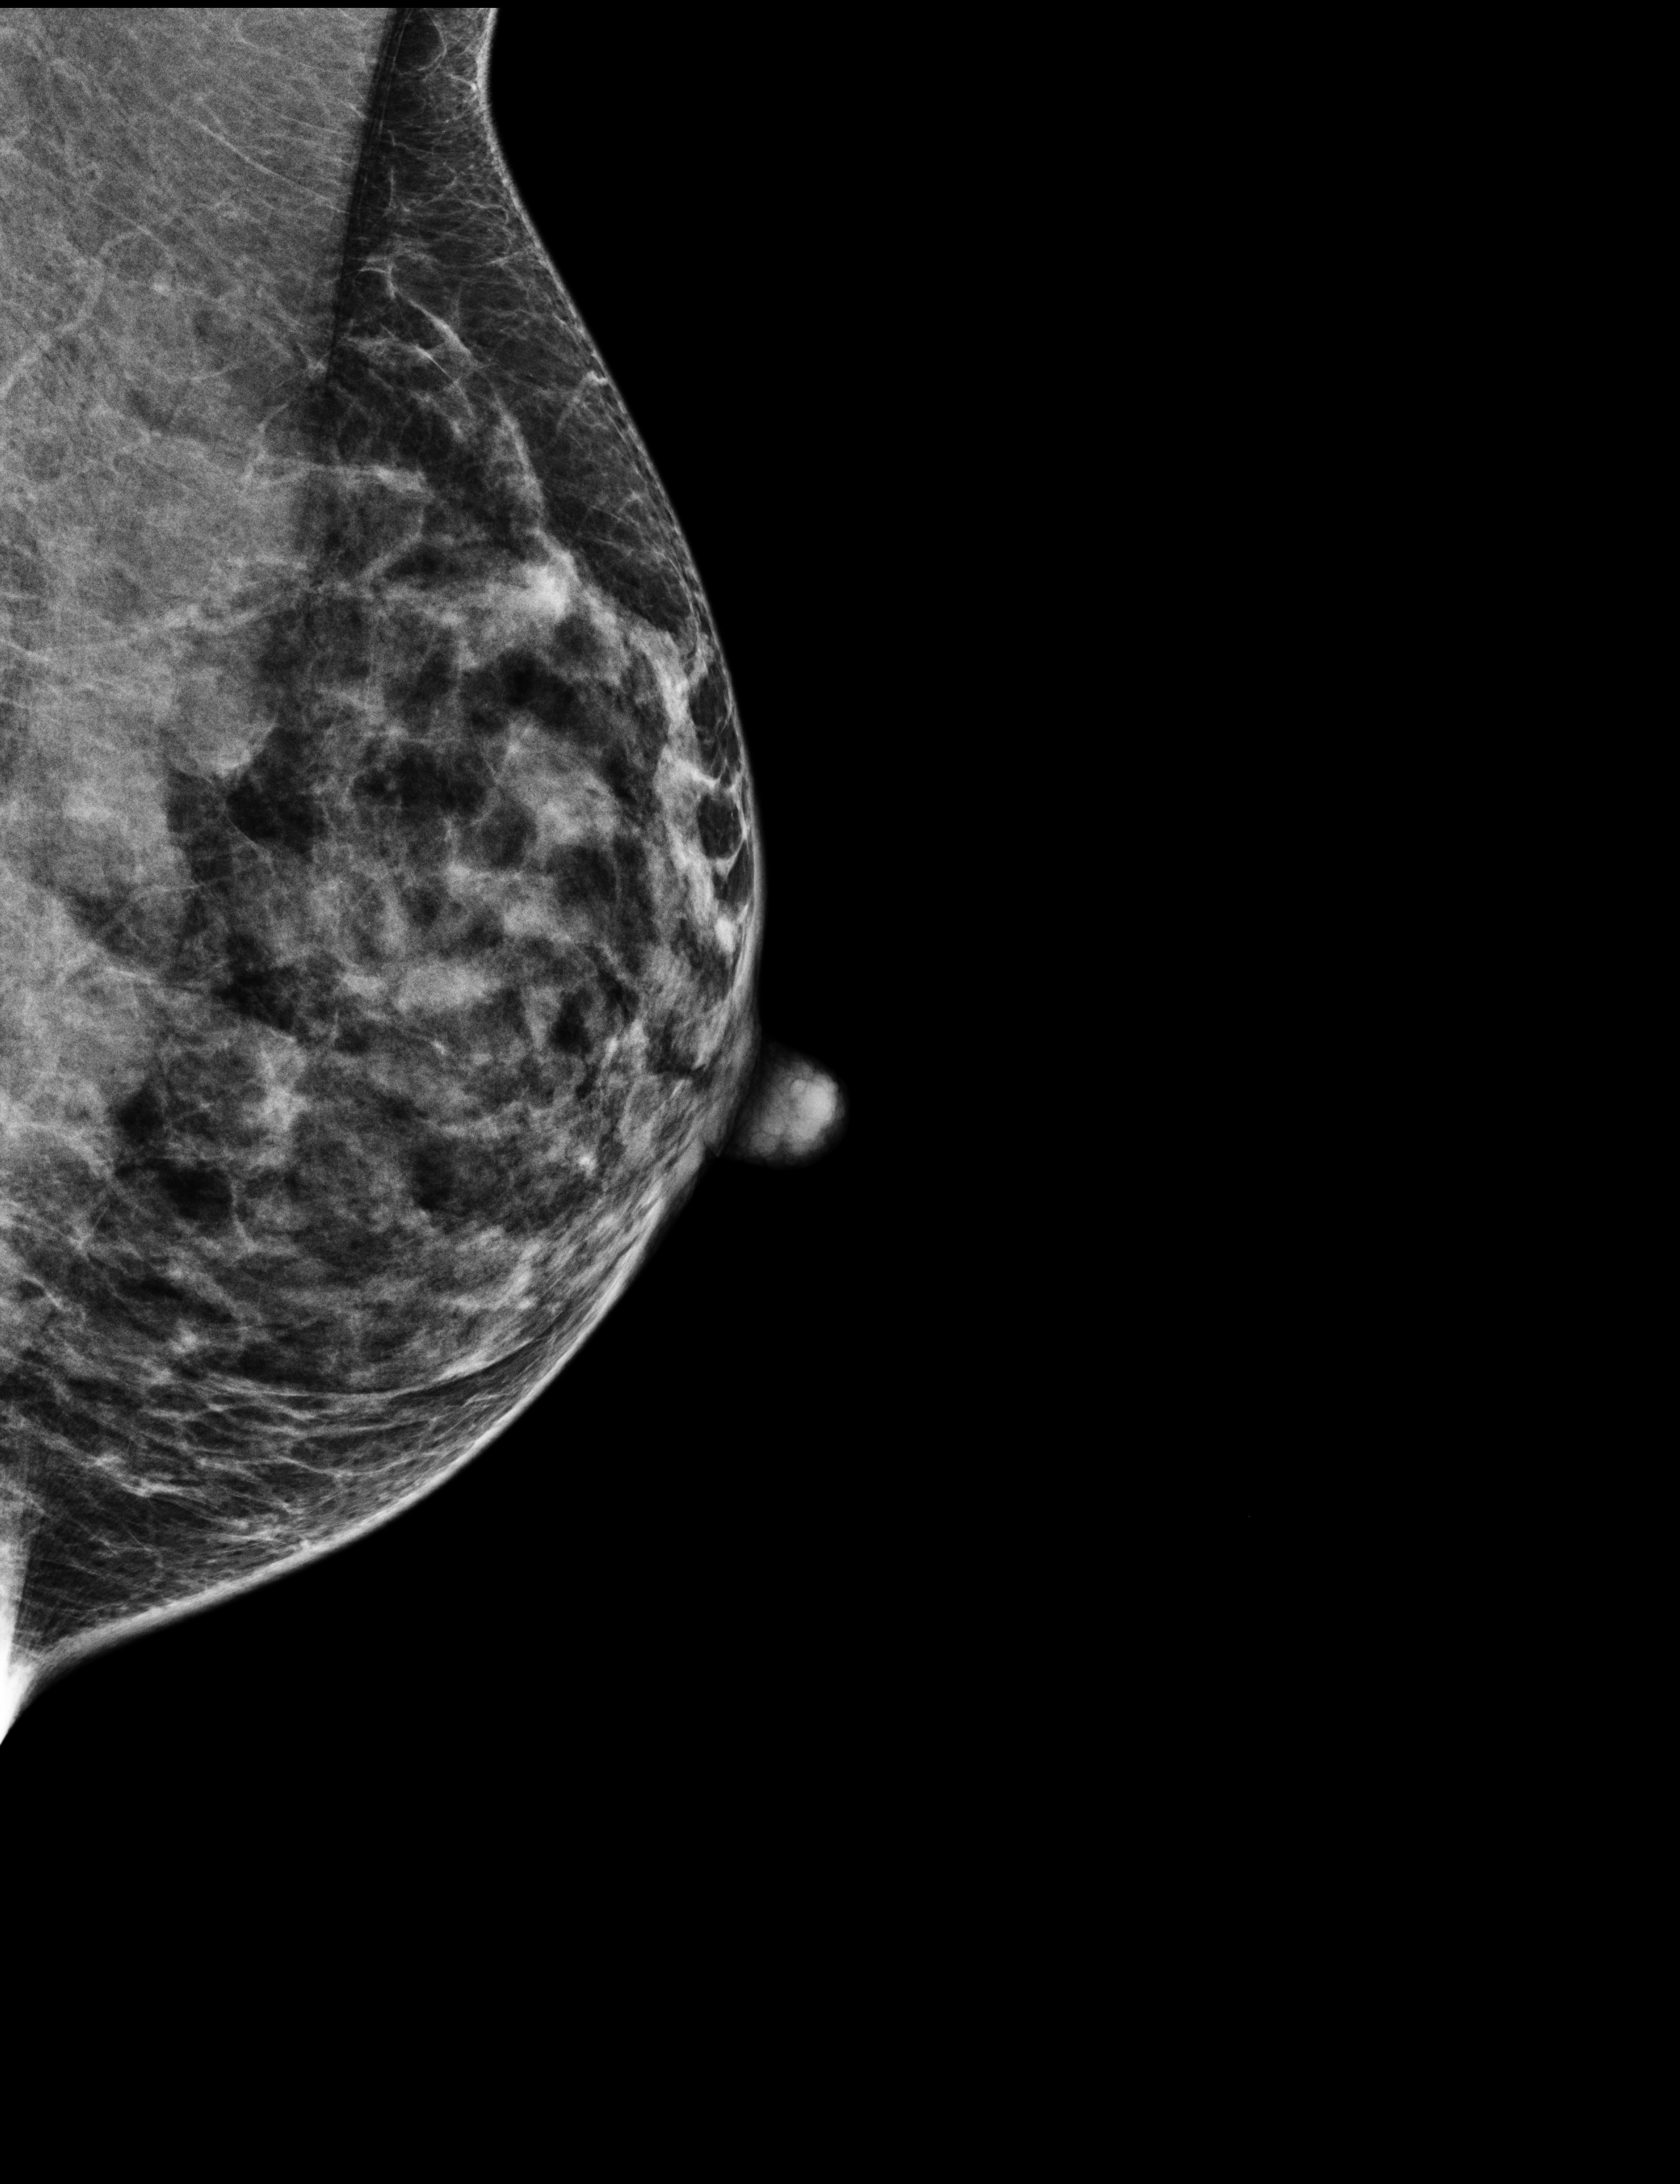
Screening examination; compressed breast thickness 35 mm. Female patient, age 54 years.
Image type: full-field digital mammogram. Breast: left. Projection: medio-lateral oblique projection.